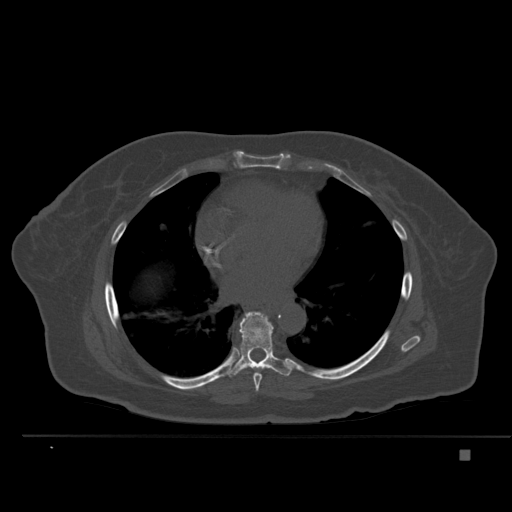
CT including the spine, one axial slice; position 315 of 477 along the scan axis; bone window (W 1800 / L 400 HU); 1.5 mm slice thickness; 512 × 512 image matrix. Patient: female, 74 years. Case-level facts recorded for this patient, not image findings: primary cancer: colon.
Structures marked on this image (semi-automatic segmentation, software-assisted and operator-edited):
- T6 vertebra: bounding box [x1, y1, x2, y2] px = [252, 311, 268, 318]
- T7 vertebra: [253, 373, 262, 391]
- T8 vertebra: [227, 312, 291, 377]